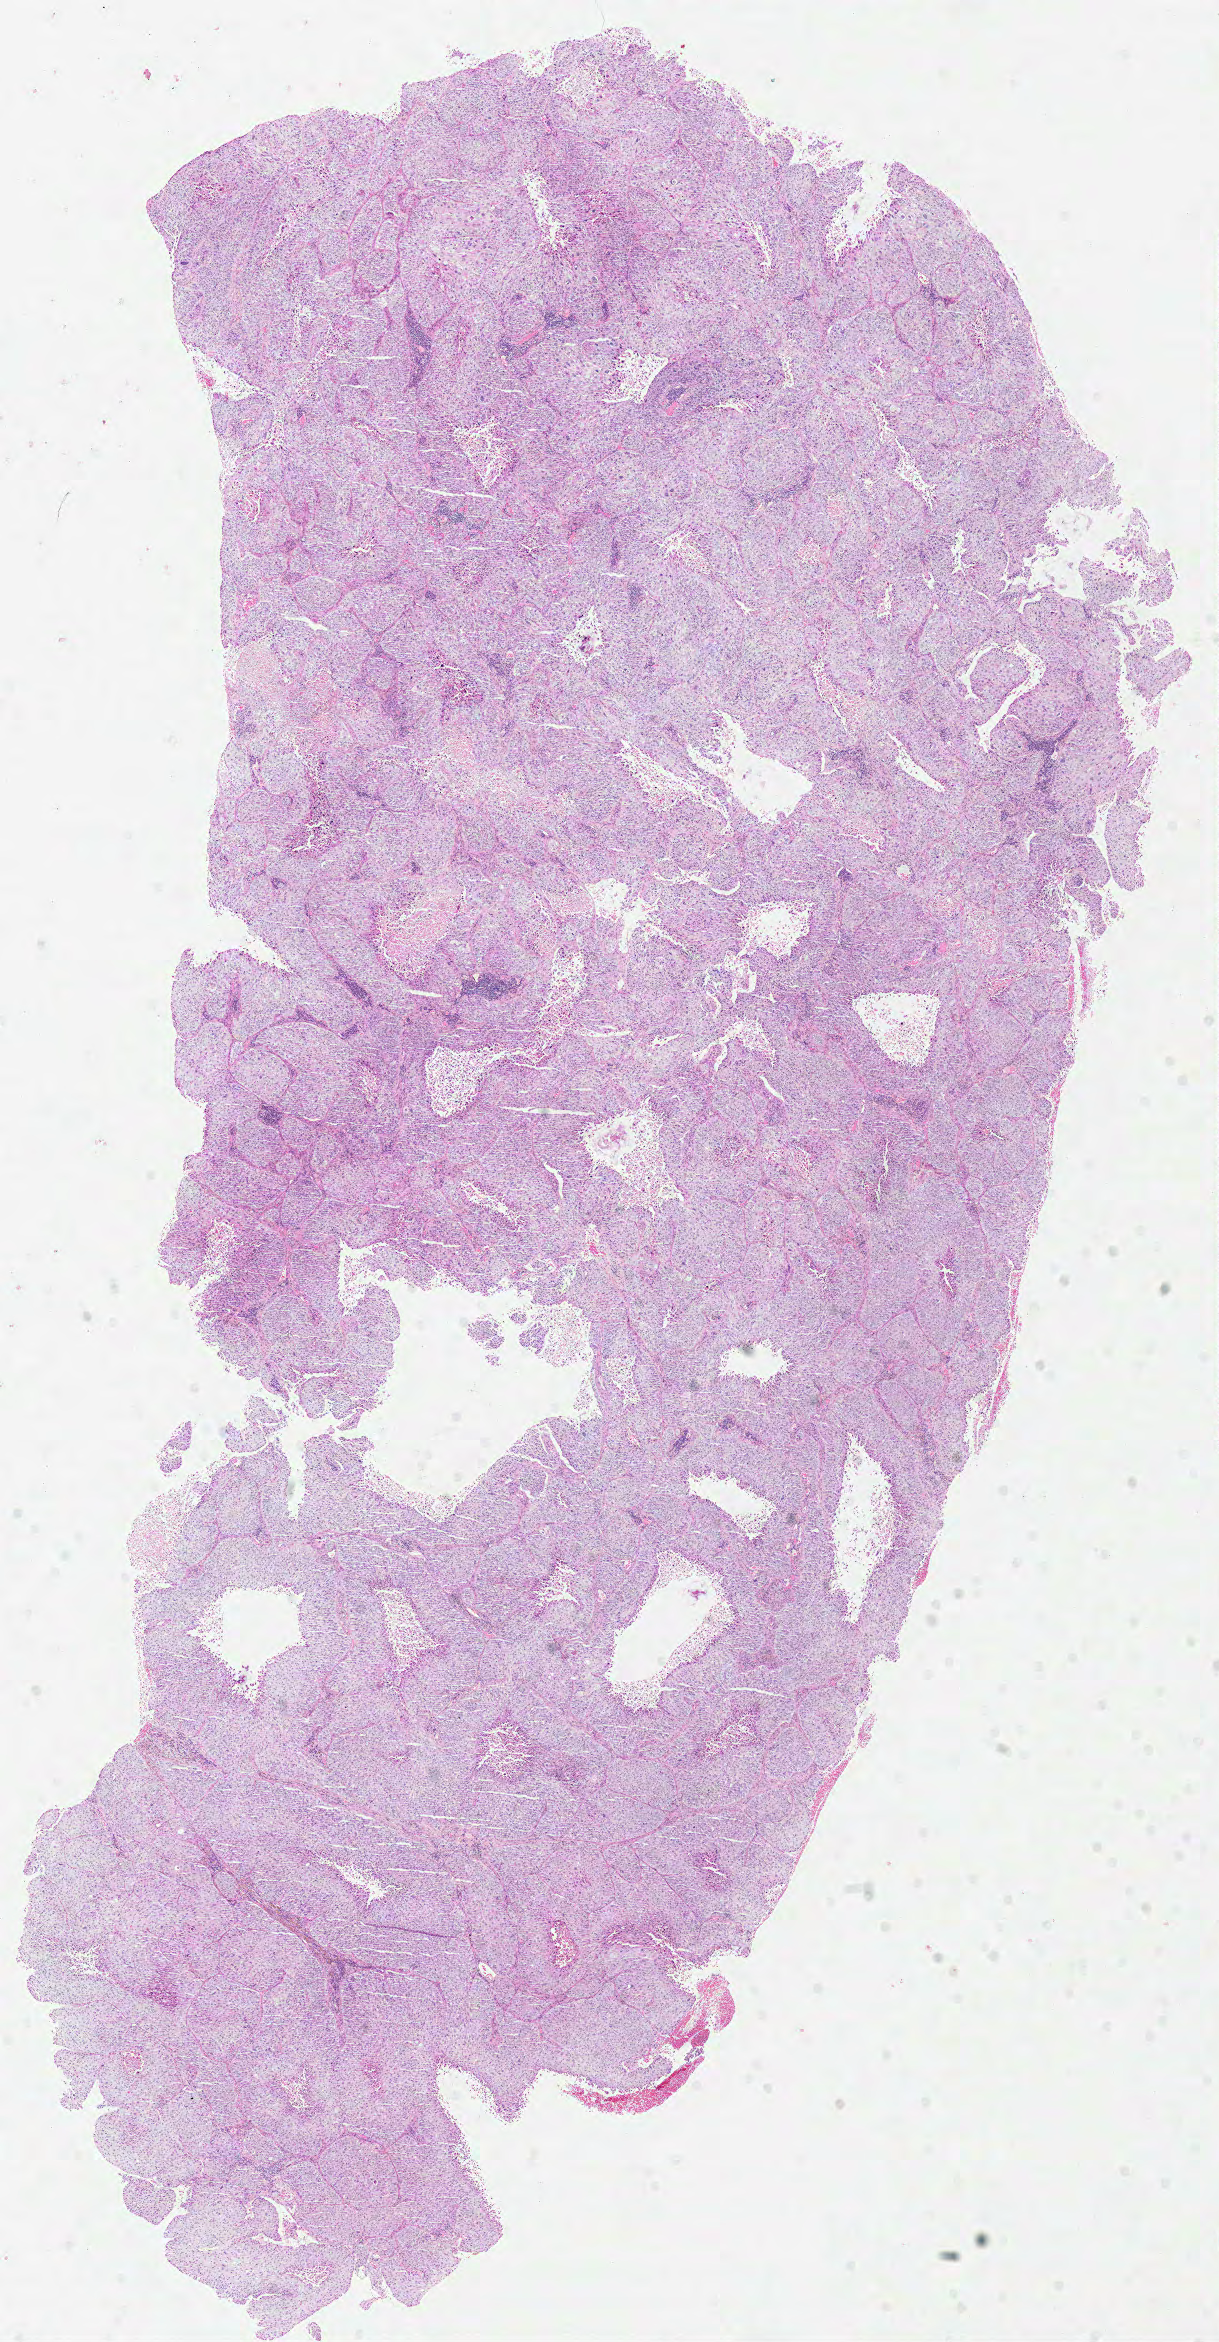
Whole-slide histology image, Hematoxylin and eosin (H&E) stained — whole scanned area (about 9.6 x 18.5 mm) shown as a low-resolution overview. Formalin-fixed paraffin-embedded (FFPE) diagnostic section. Primary tumour sample from the lung. Male patient; age at initial diagnosis 54 years.
• diagnosis: Squamous cell carcinoma, NOS (upper lobe, lung)
• AJCC pathologic stage: IIIA
• laterality: left
• TNM: T2 N2 M0